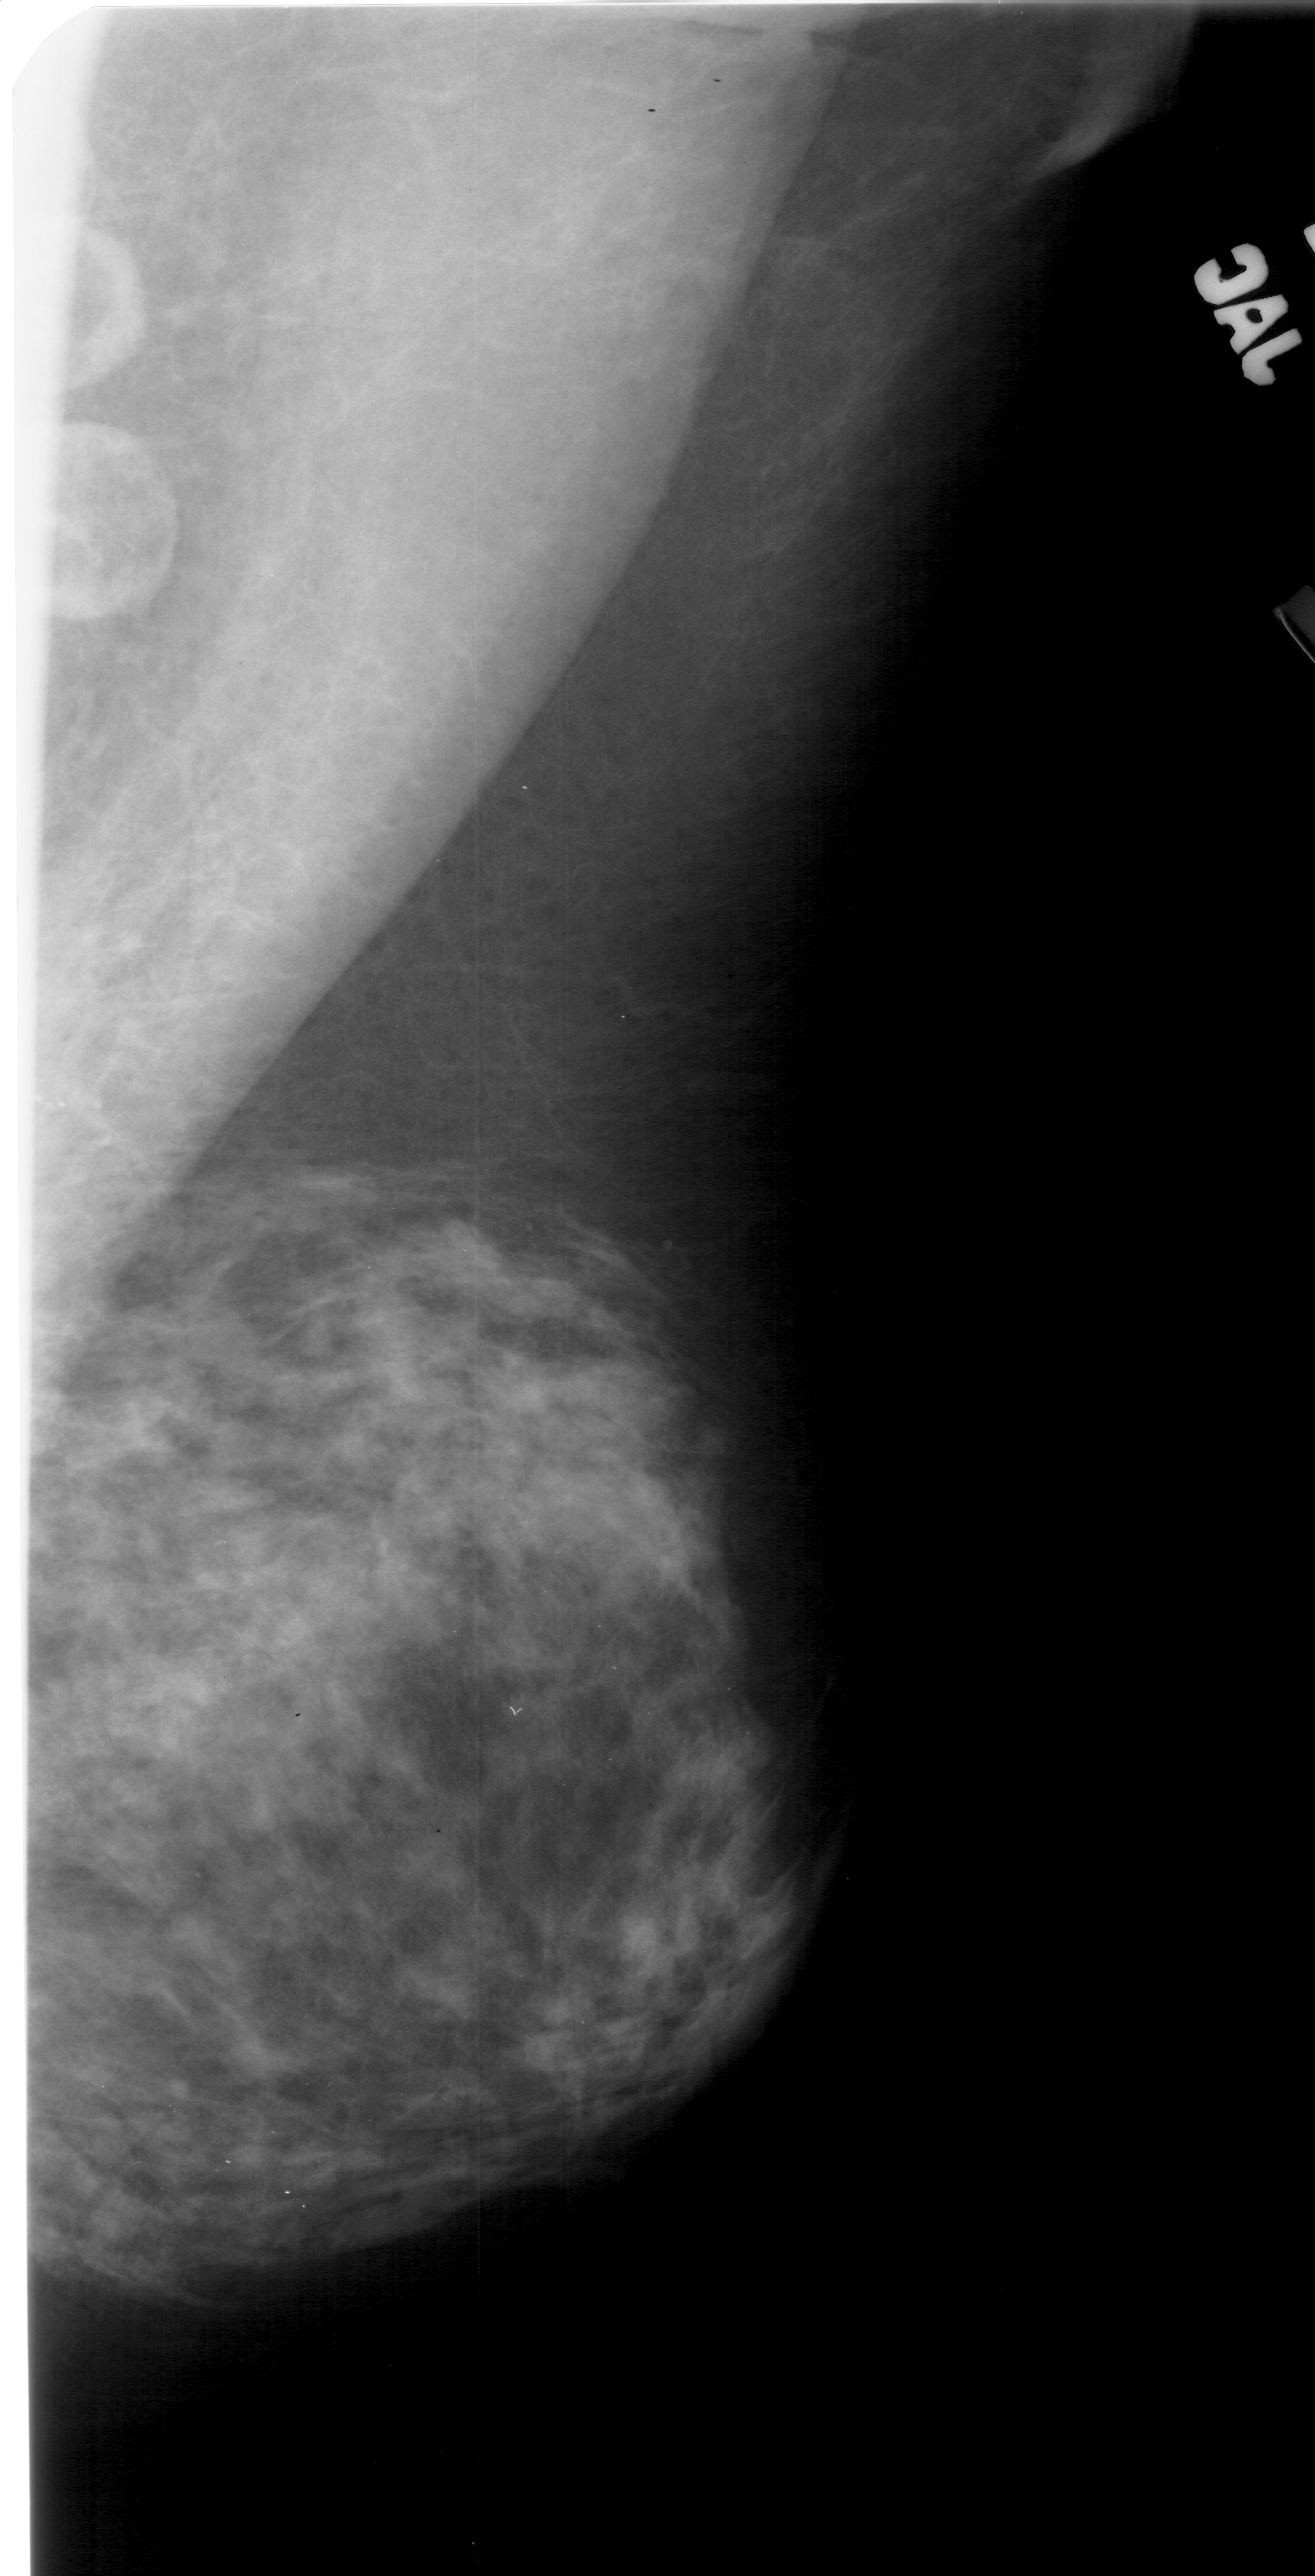
Digitized screen-film mammogram, right breast, MLO view.
Radiologist-marked abnormalities on this image: calcifications, morphology pleomorphic, distribution clustered; BI-RADS assessment category 4; subtlety rating 2 on a 1 (subtle) to 5 (obvious) scale; pathology (as recorded): benign.